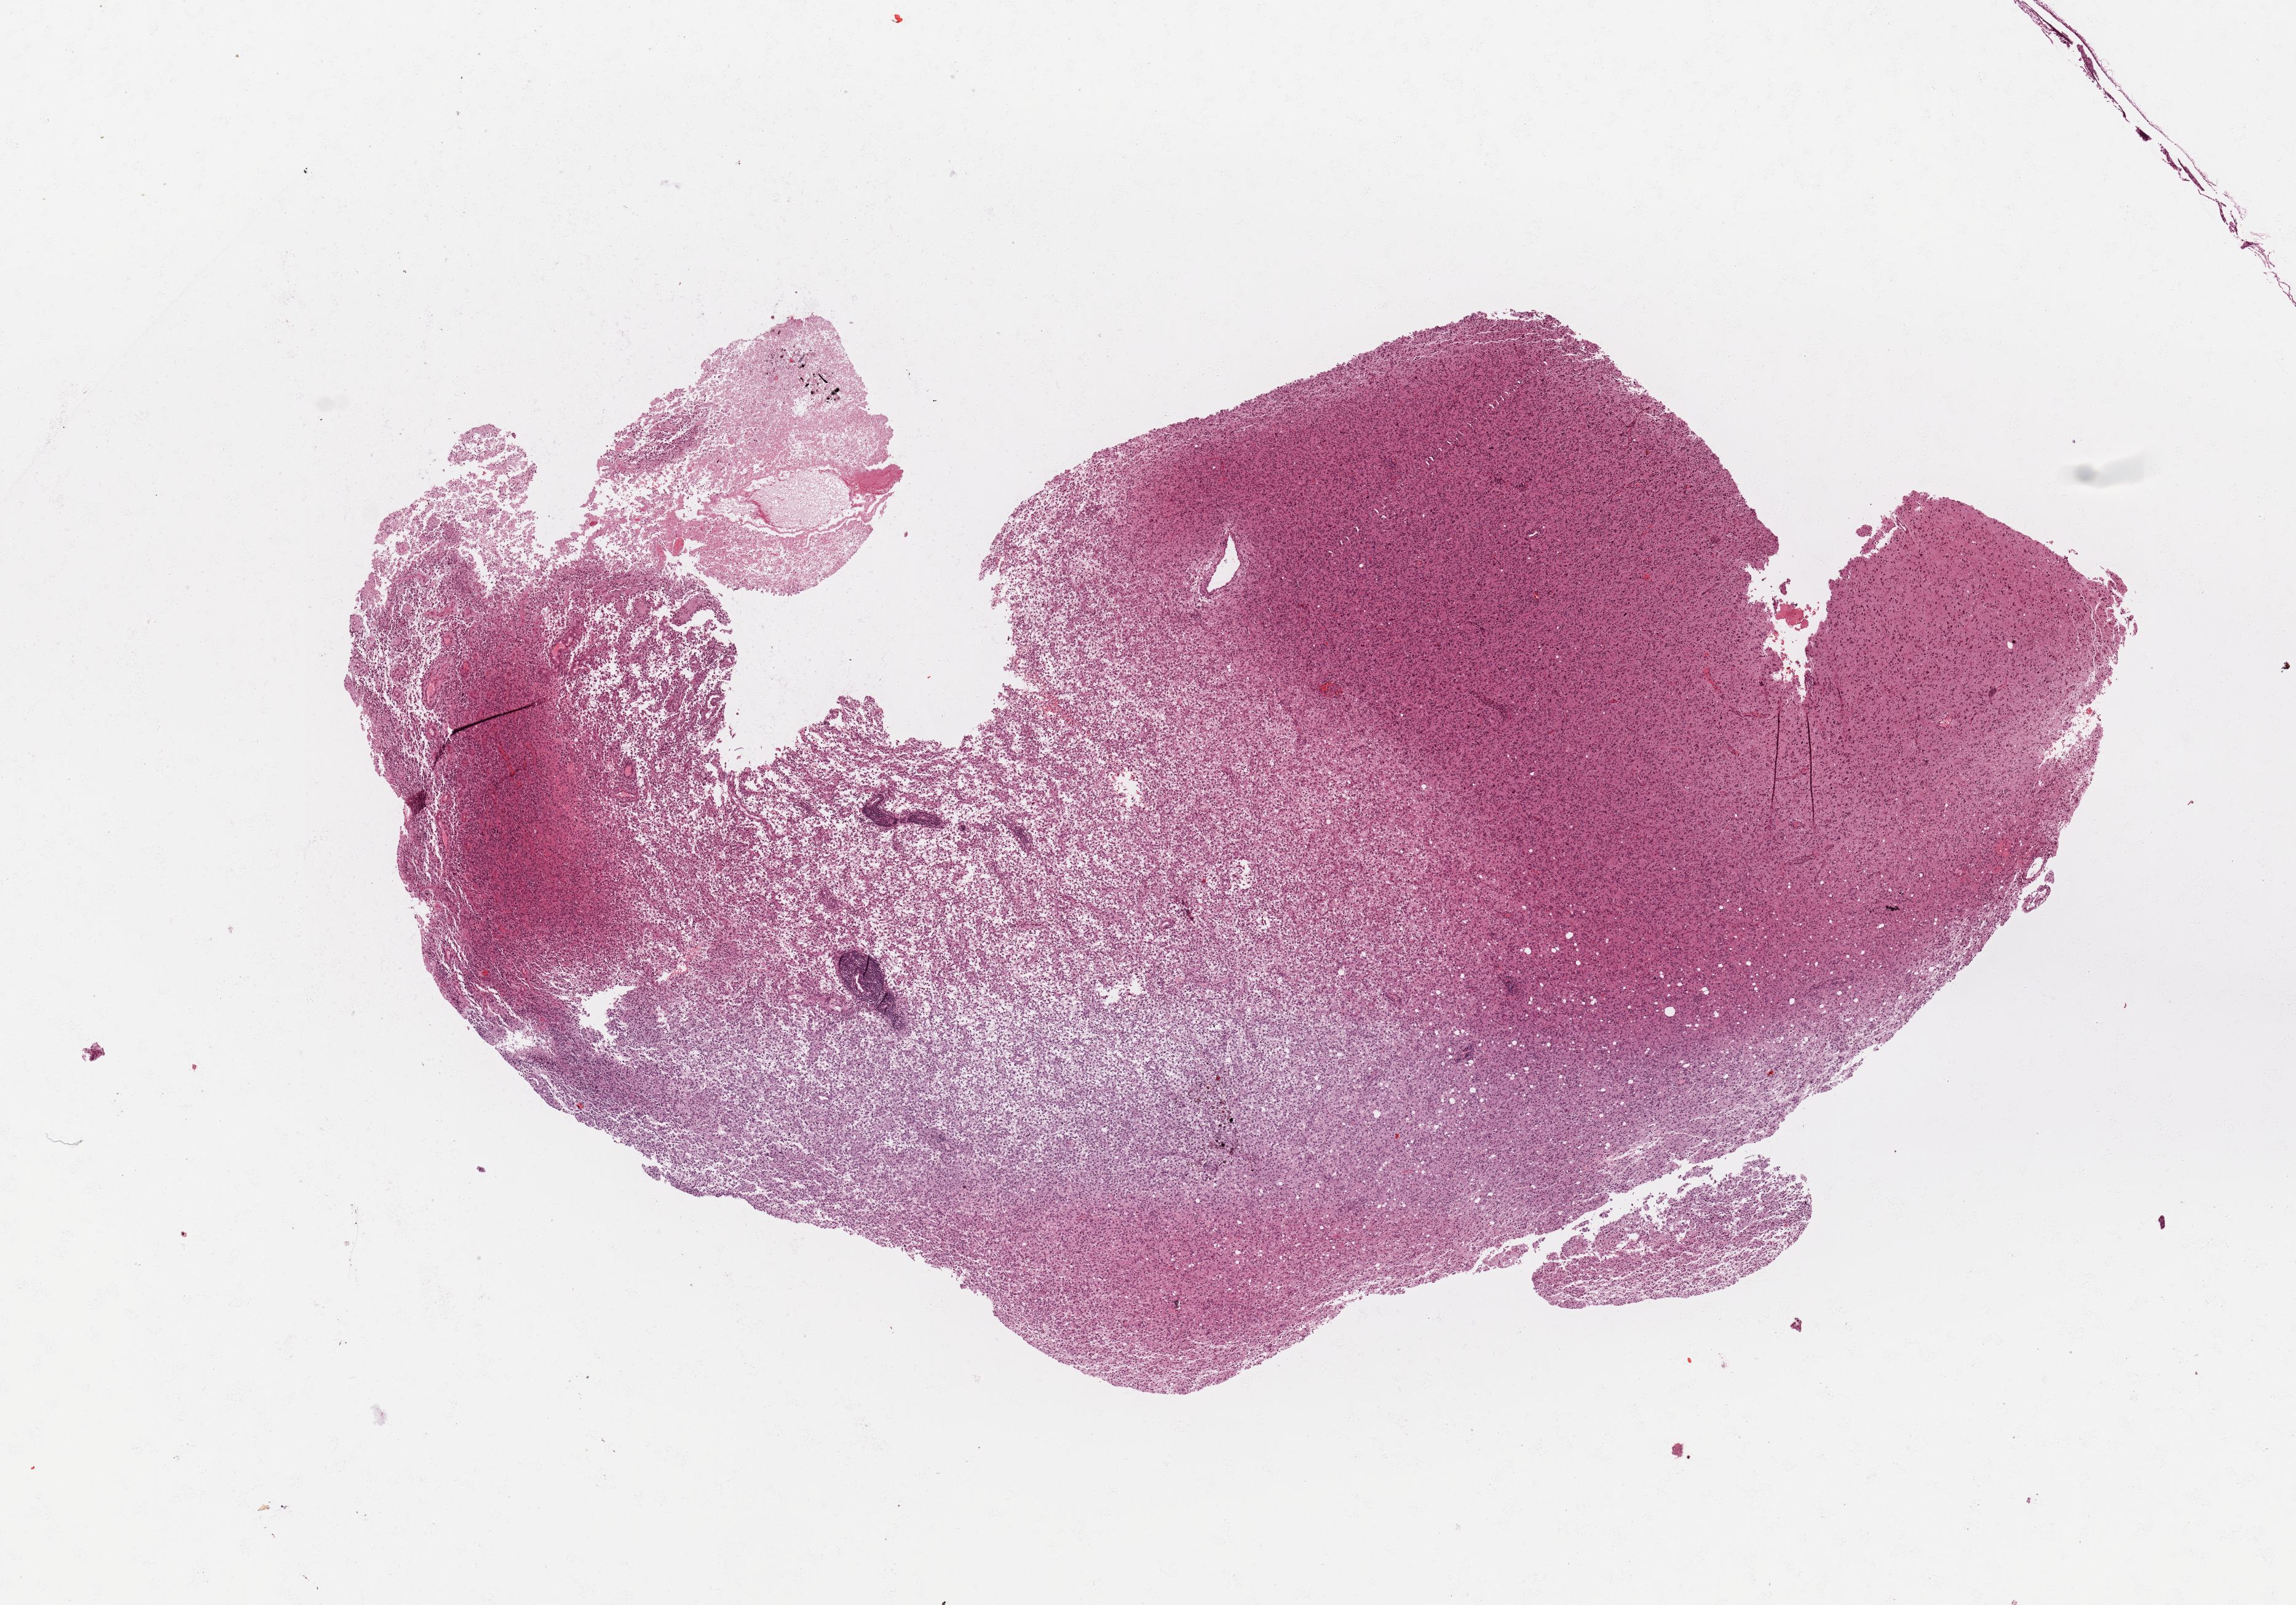
Digitized H&E-stained tissue section (whole slide) — a low-resolution overview of the entire scanned area, about 14.8 x 10.3 mm; tumour tissue sample, sampled site: frontal lobe. Male, 44 y/o. Slide review estimates, as recorded: tumour nuclei 85%, necrosis 5%.
- histologic diagnosis: Glioblastoma
- primary tumour site (as recorded): frontal lobe